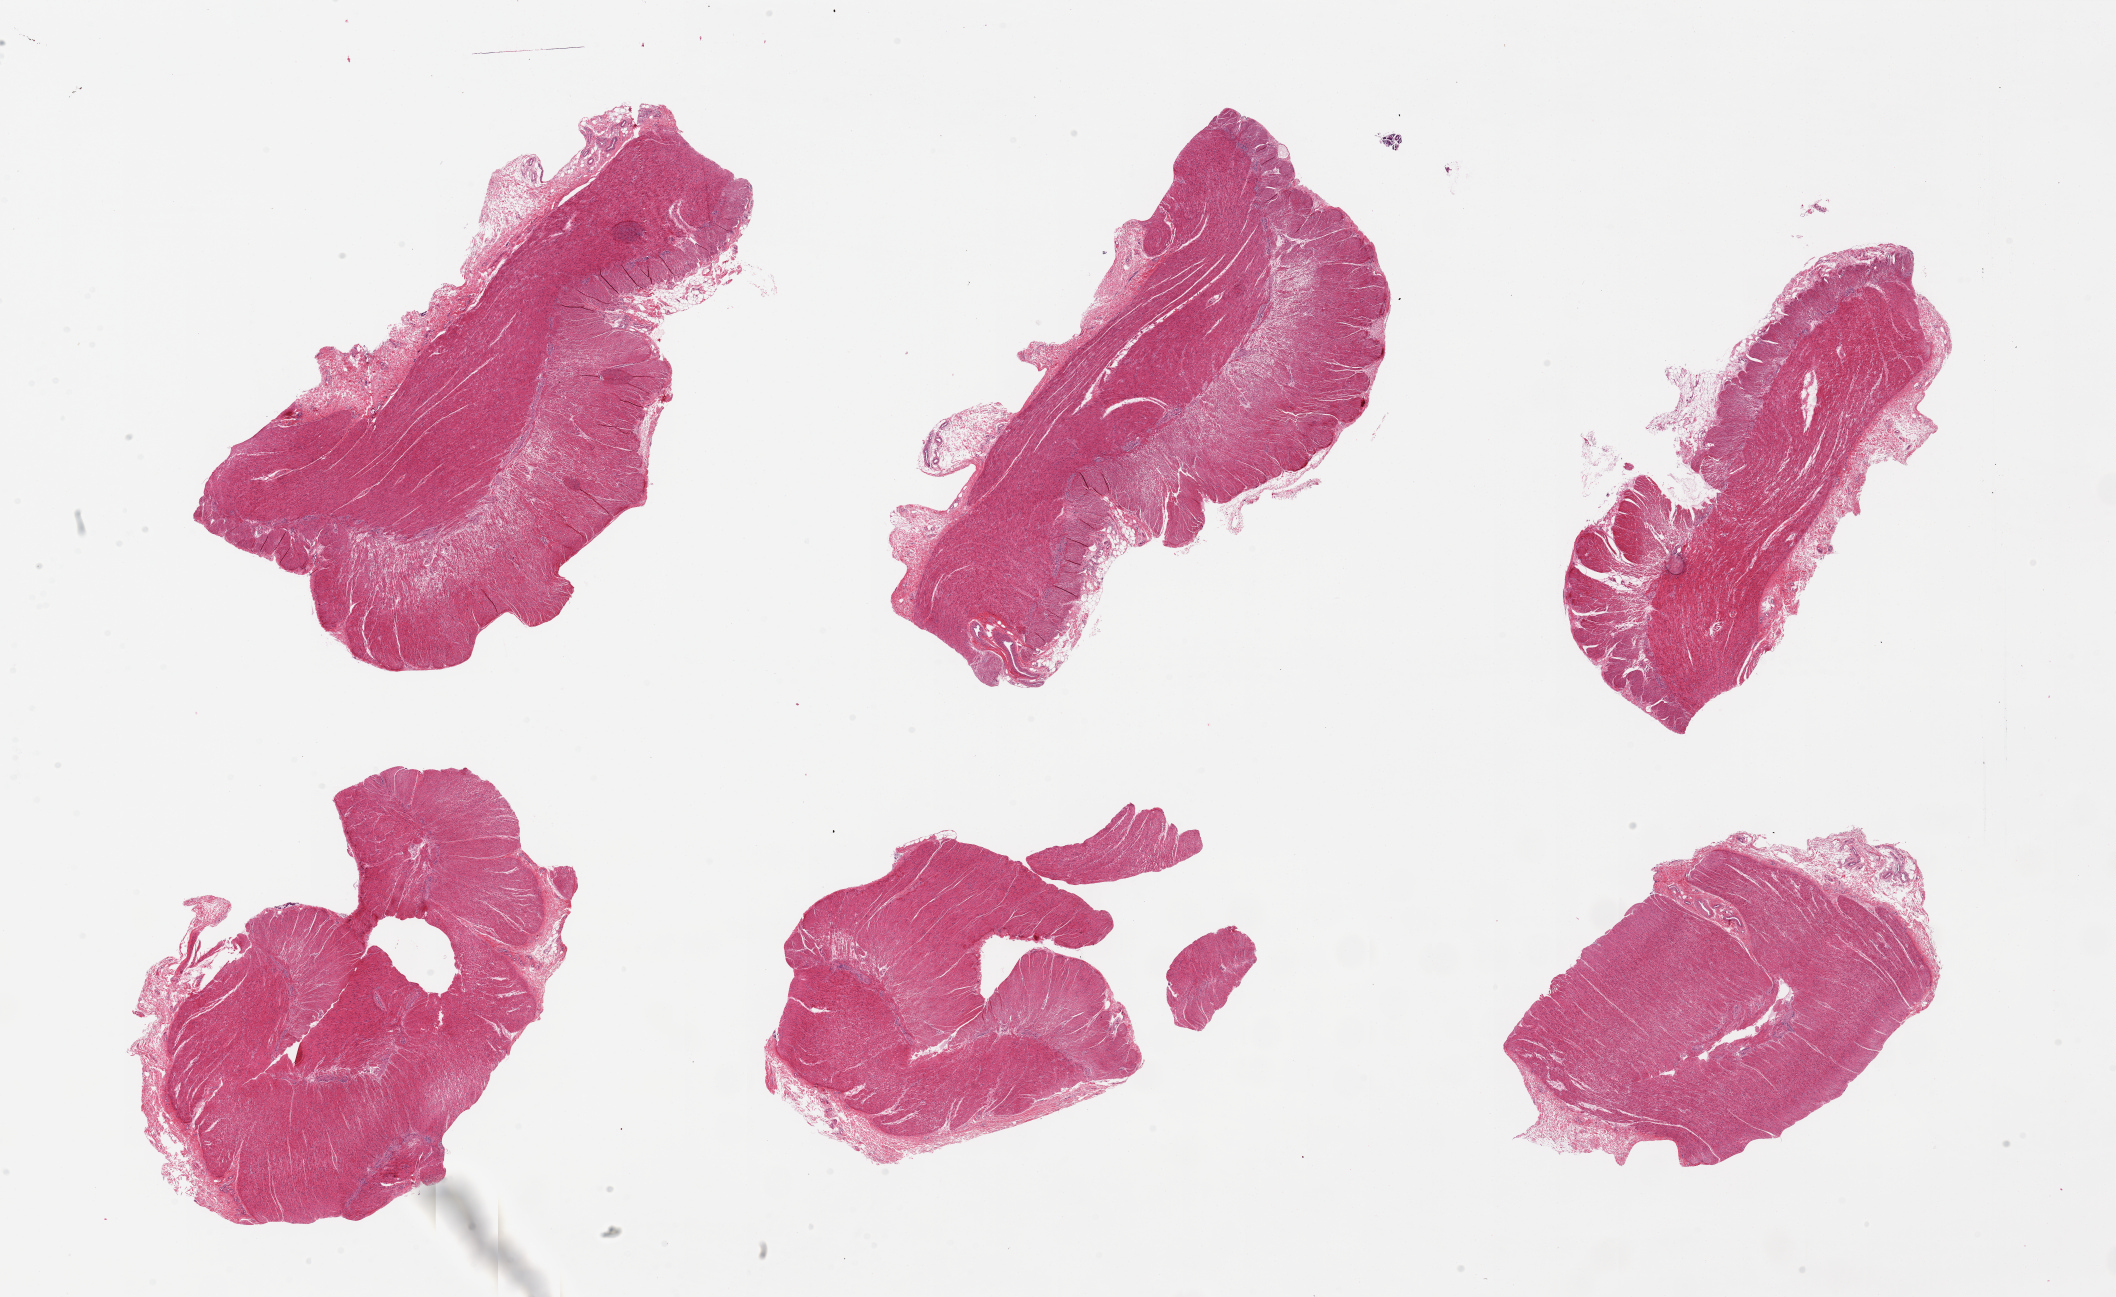
Whole-slide image, haematoxylin and eosin stain, brightfield, a low-resolution overview of the entire scanned area, about 33.5 x 20.5 mm; PAXgene-fixed paraffin-embedded (PFPE) section; sampled site (target tissue): sigmoid colon; donor tissue sample.
Review note (as recorded): 6 pieces, up to 10x6mm; all muscularis; good specimens.